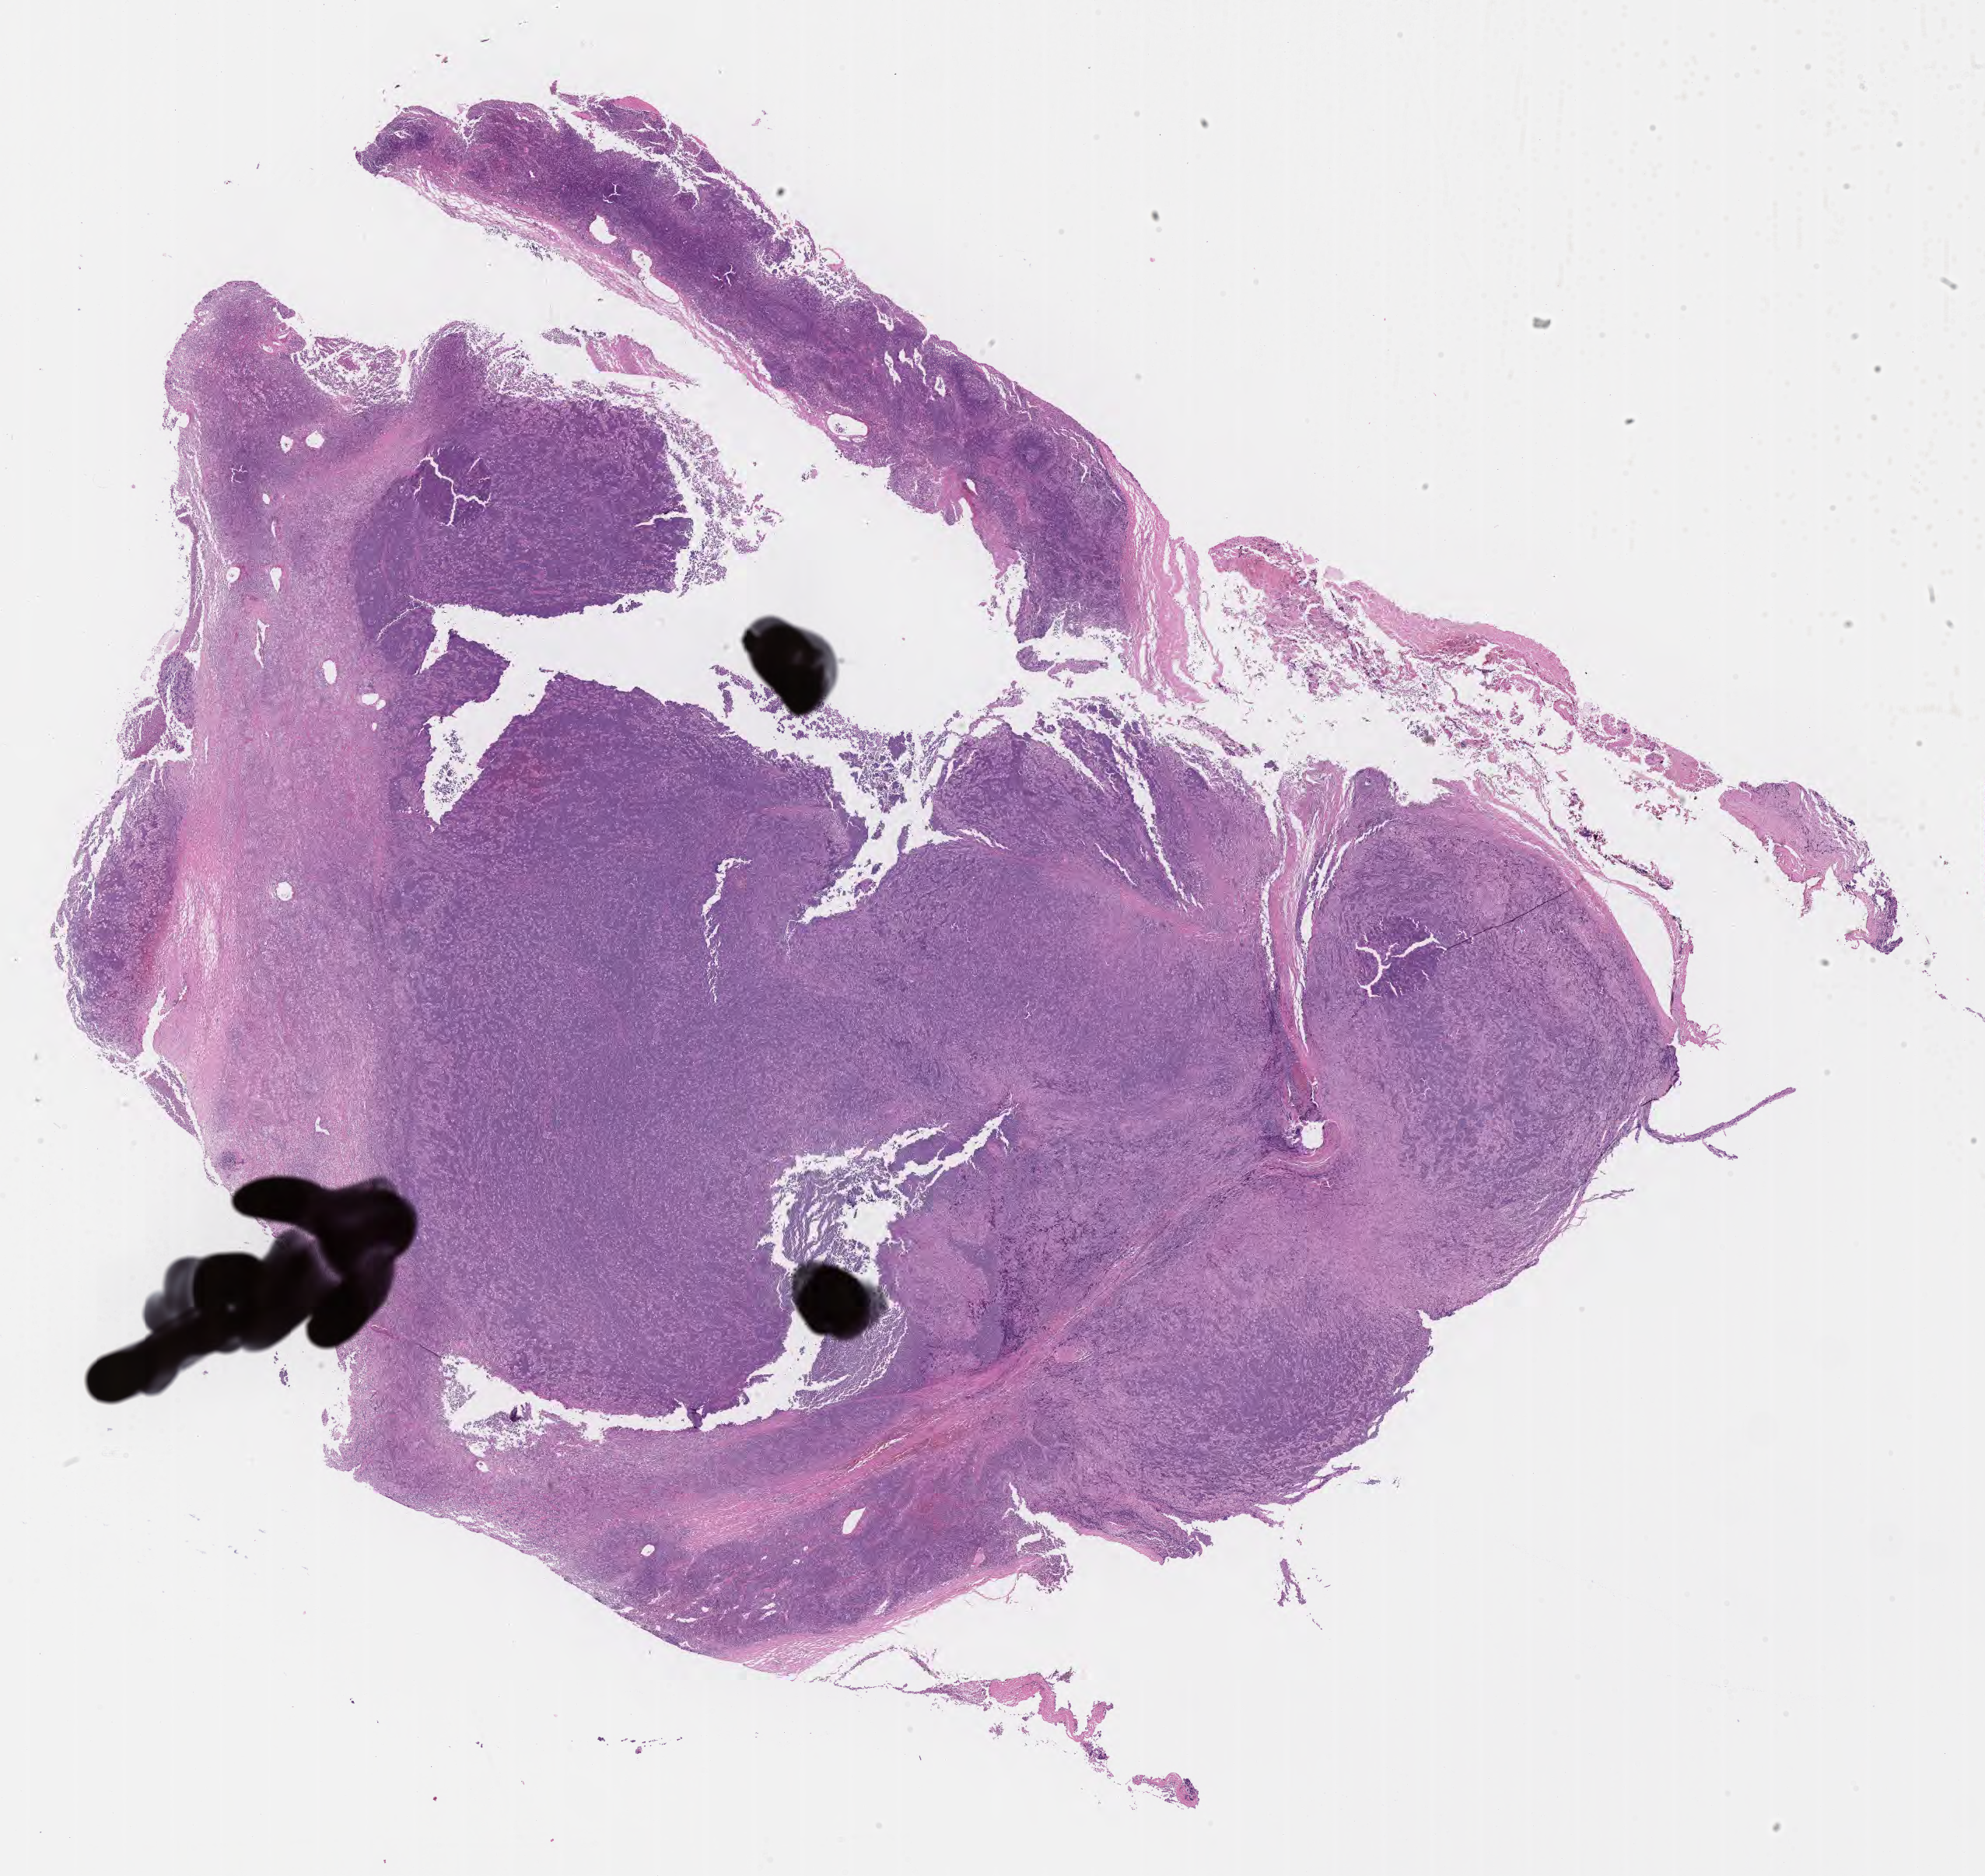
Haematoxylin and eosin whole-slide image, whole scanned area (about 20.6 x 19.5 mm) shown as a low-resolution overview; tumor tissue. Patient: male, age at initial diagnosis 4 years.
* diagnosis: Burkitt lymphoma, NOS